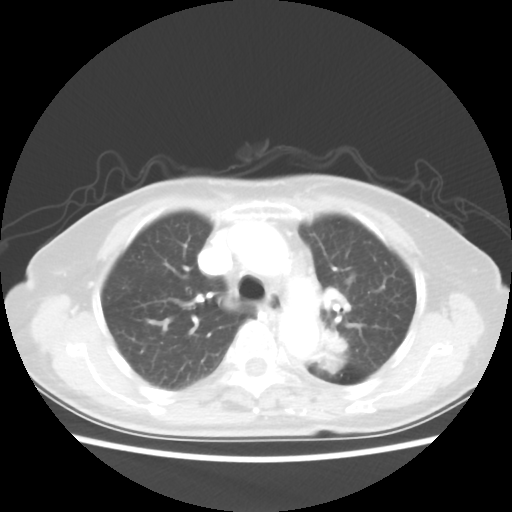
Chest CT, one axial slice. Position 34 of 50 along the scan axis. Reconstruction kernel STANDARD. Lung window (W 1500 / L -600 HU). 5 mm slice thickness. 512 × 512 image matrix, field of view 335 × 335 mm. Female patient, age 81 years. Case-level facts recorded for this patient, not image findings: clinical TNM (as recorded): T2 N0 M1a.
Outlined on this slice (bounding box drawn by a radiologist):
- lung tumour (recorded histology: squamous cell carcinoma): bounding box <312,324,345,374> (left, top, right, bottom; pixels)